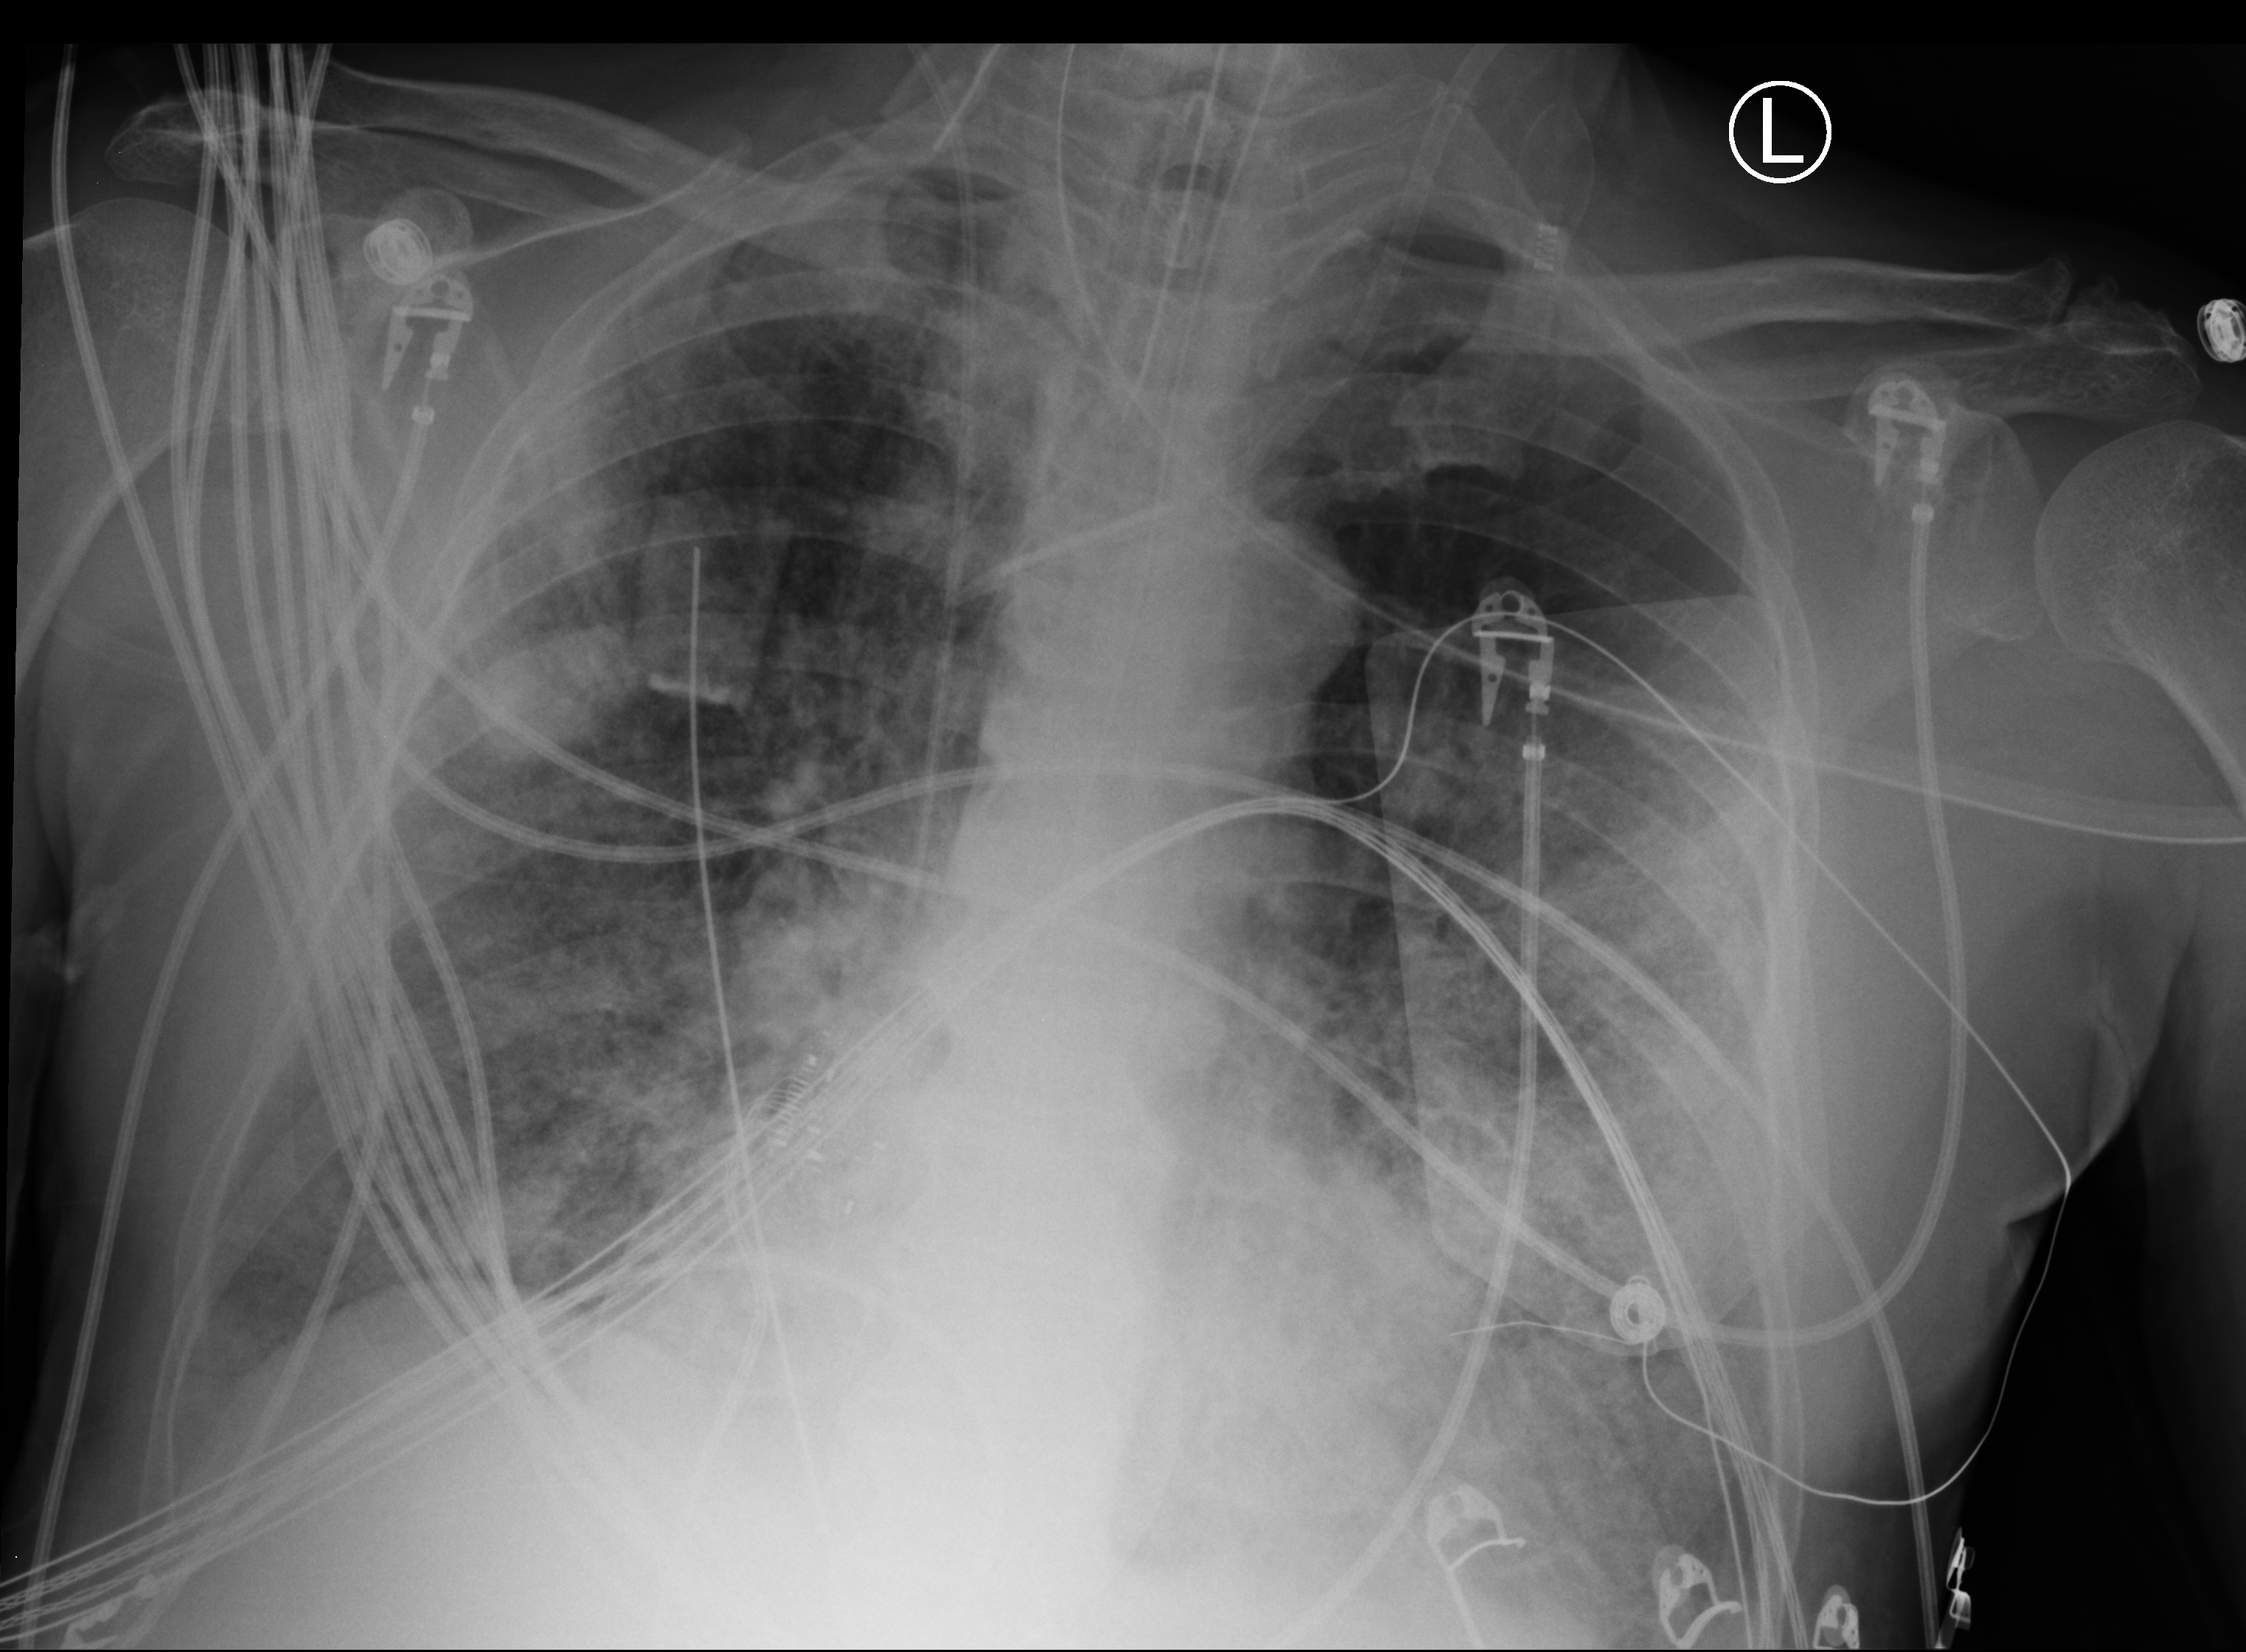
Chest X-ray (portable); anteroposterior (AP) projection. Male patient hospitalised with COVID-19, age 60–74 years.
From the hospital-stay record, not from the radiograph (when in the stay this image was taken is not recorded):
- admitted to intensive care during this hospital stay: yes
- mechanically ventilated during this hospital stay: yes
- length of hospital stay: 26 days